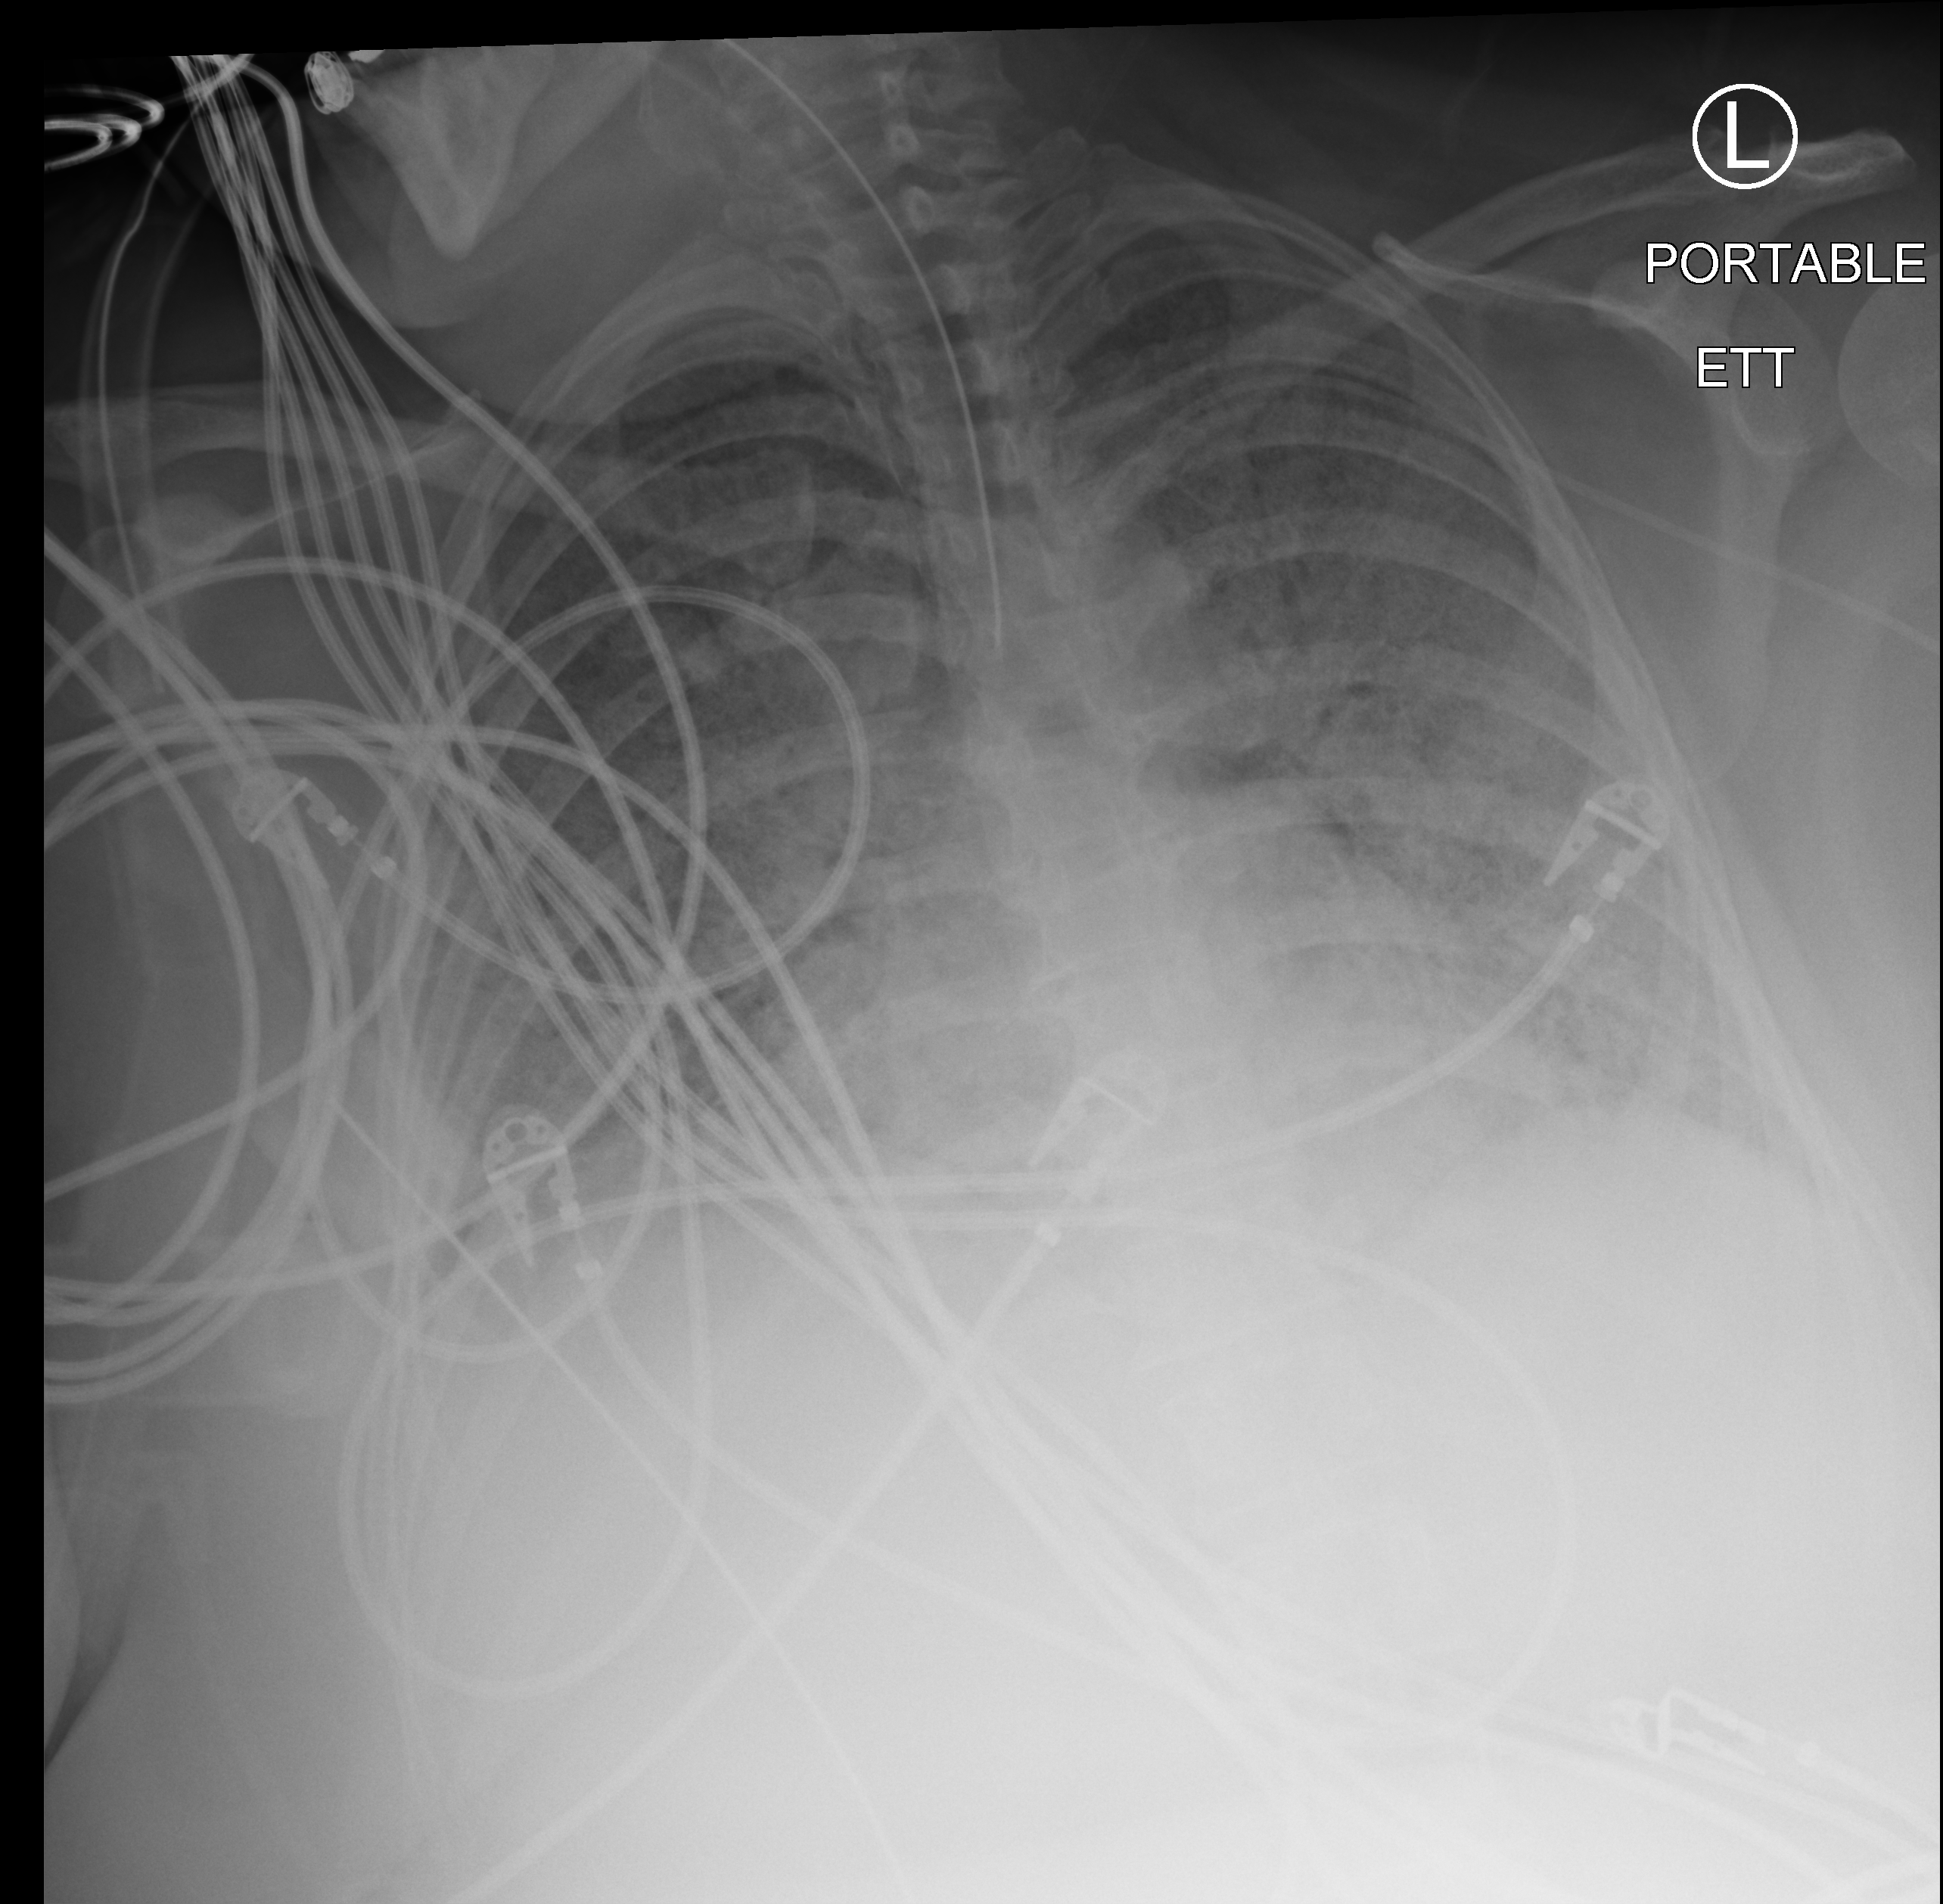
Chest X-ray (portable); anteroposterior (AP) projection. Patient hospitalised with COVID-19; female, aged 18–59 years.
Hospital-stay facts (about this admission, not read from this image; timing relative to this image not recorded): mechanically ventilated during this hospital stay: yes; COPD (admission record): no.